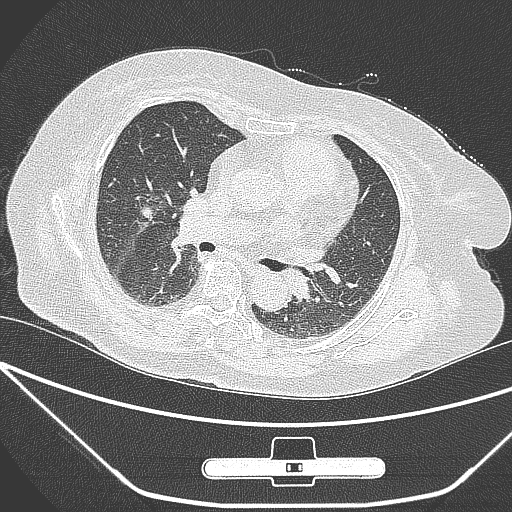
Chest CT, one axial slice; lung window (W 1500 / L -600 HU); 1 mm slice thickness; 512 × 512 image matrix, field of view 365 × 365 mm. Female patient, age 65 years. From the clinical record (not read from this slice): clinical TNM (as recorded): T1c N0 M0; histopathological grade: G3.
Annotated regions visible in this slice (bounding box drawn by a radiologist):
- lung tumour (recorded histology: adenocarcinoma): bounding box [x1, y1, x2, y2] px = [139, 200, 163, 230]